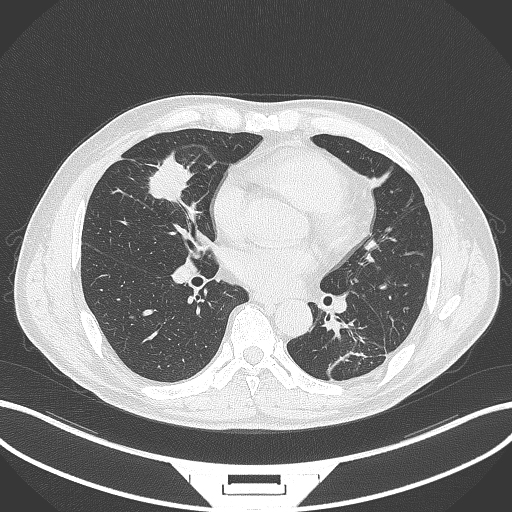
Chest CT, one axial slice. Slice 137 of 399 in the series (ordered by position). Reconstruction kernel B70f. 120 kVp. Lung window (W 1500 / L -600 HU). 1 mm slice thickness. 512 × 512 image matrix, field of view 400 × 400 mm. Patient: male, 59 years. Case-level facts recorded for this patient, not image findings: clinical TNM (as recorded): T2a N1 M0.
Annotated regions visible in this slice (bounding box drawn by a radiologist):
- lung tumour (recorded histology: adenocarcinoma): box from (x=146, y=149) to (x=204, y=207) px